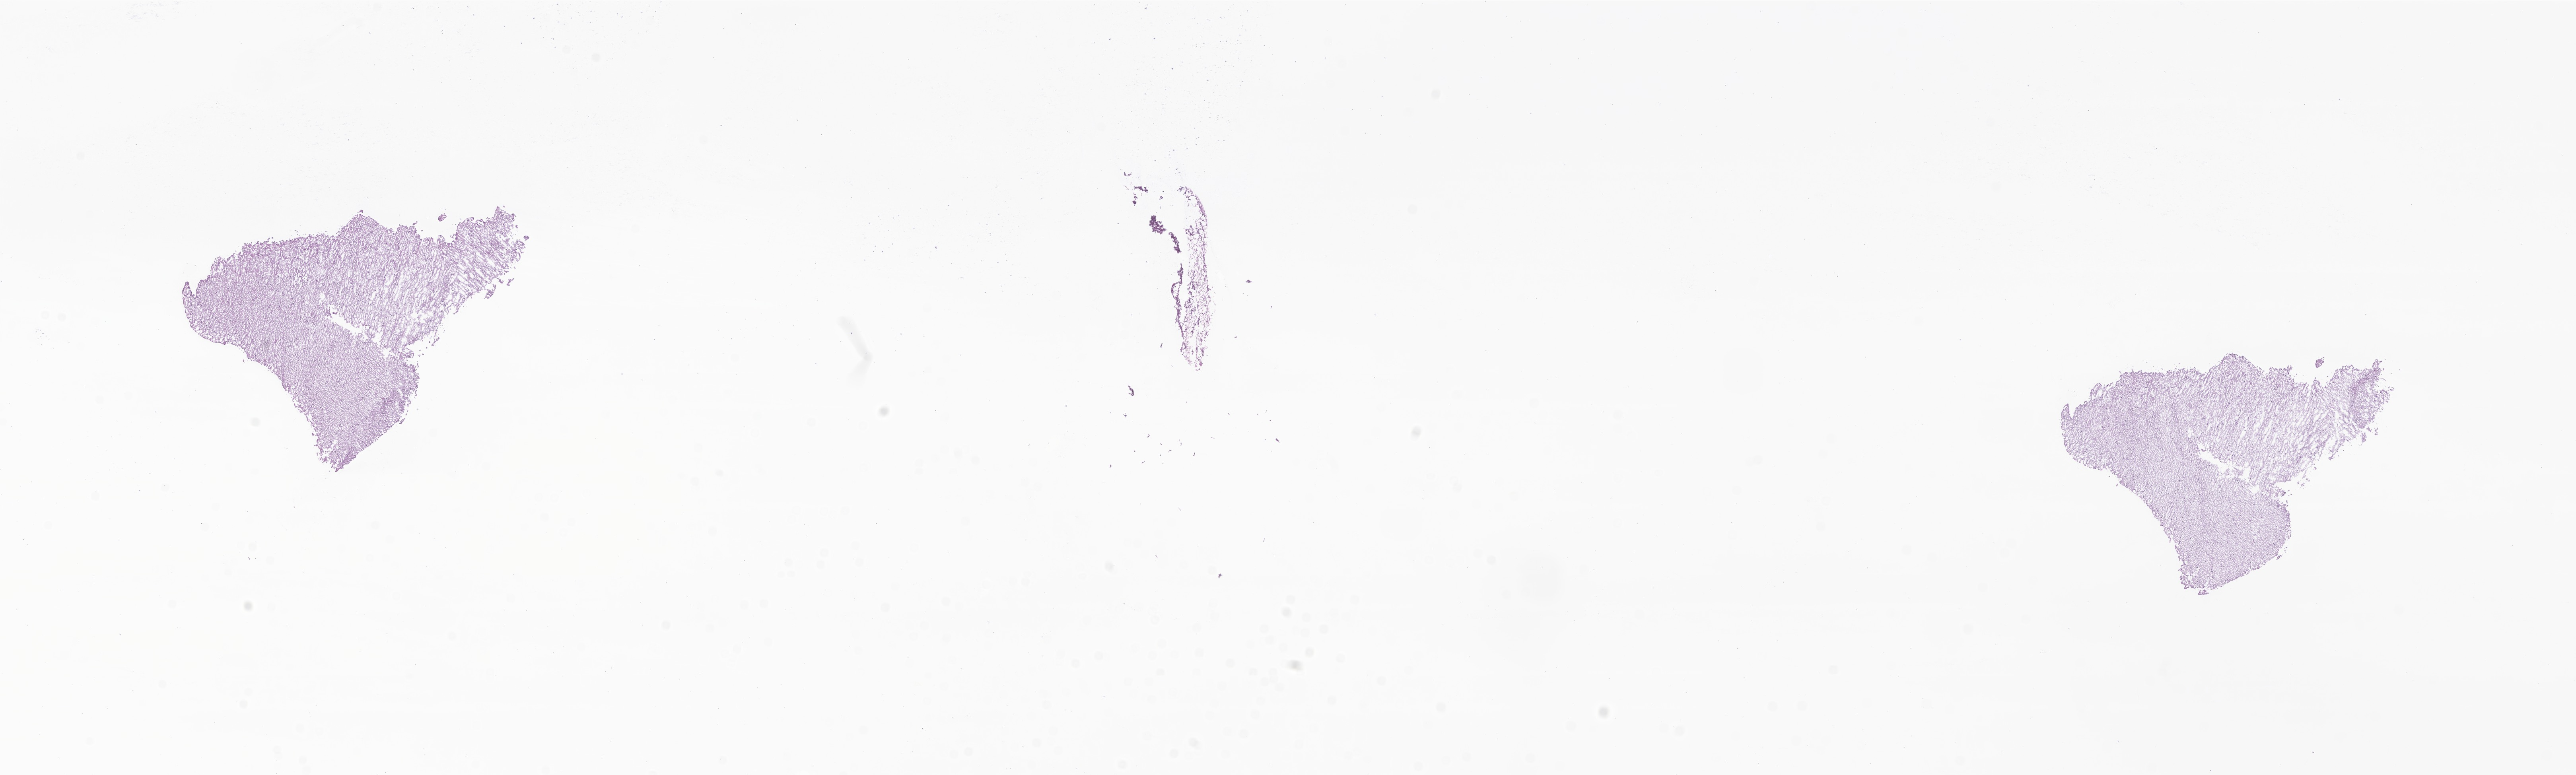
Haematoxylin and eosin whole-slide image of tumor tissue from the brain, a low-resolution overview of the entire scanned area, about 27.3 x 8.2 mm. Frozen section. Male patient, age 218 months (18 years 2 months).
Recorded diagnosis: Neoplasm, uncertain whether benign or malignant.